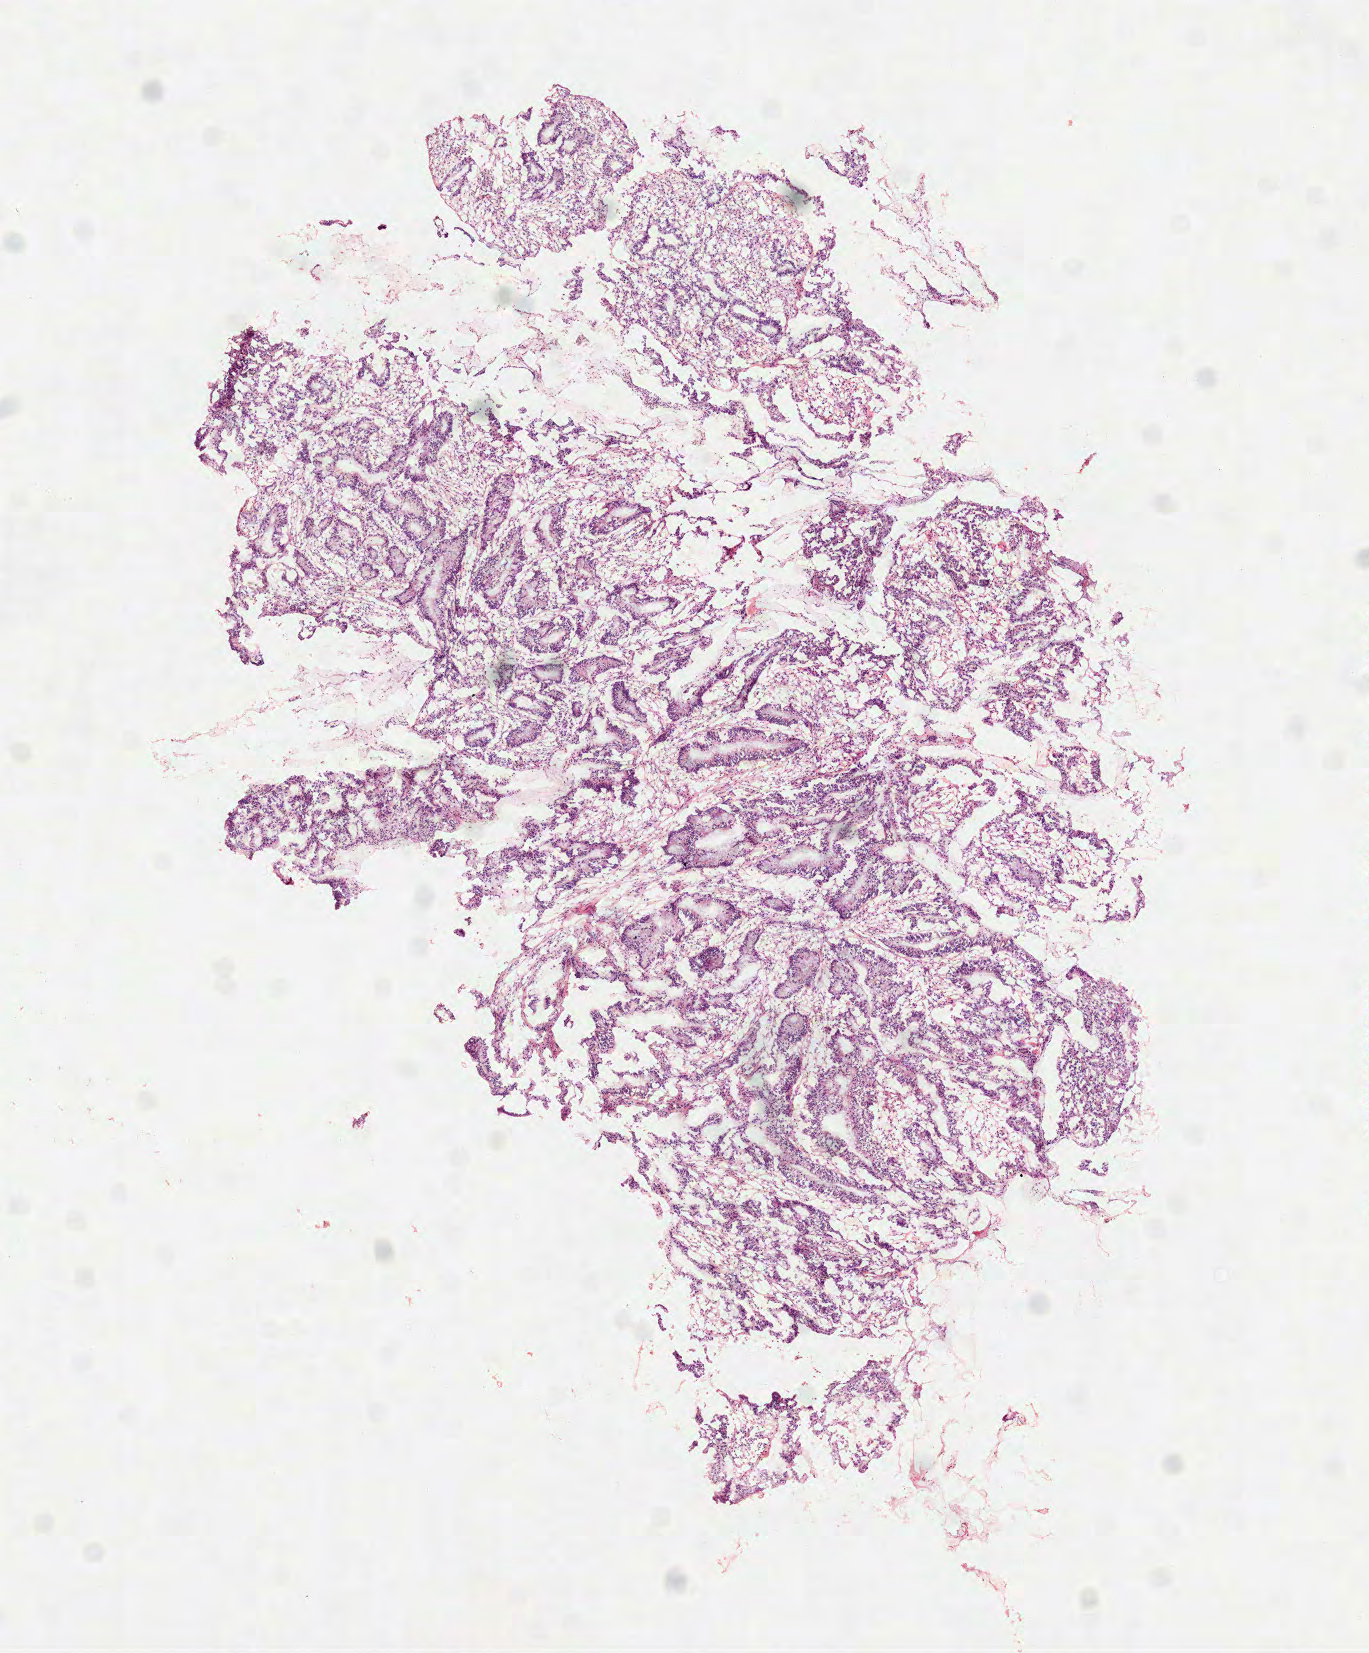
Whole-slide histology image, H&E, shown as a low-resolution overview of the whole scanned area (about 5.5 x 6.7 mm). Frozen section from the top of the tissue portion. Sample: primary tumour, colon. Female patient. Composition of this section per pathologist review: tumour cells 75%, tumour nuclei 75%, normal cells 0%, stromal cells 25%, necrosis 0%.
* pathologic diagnosis: Mucinous adenocarcinoma
* AJCC pathologic stage: I (5th edition)